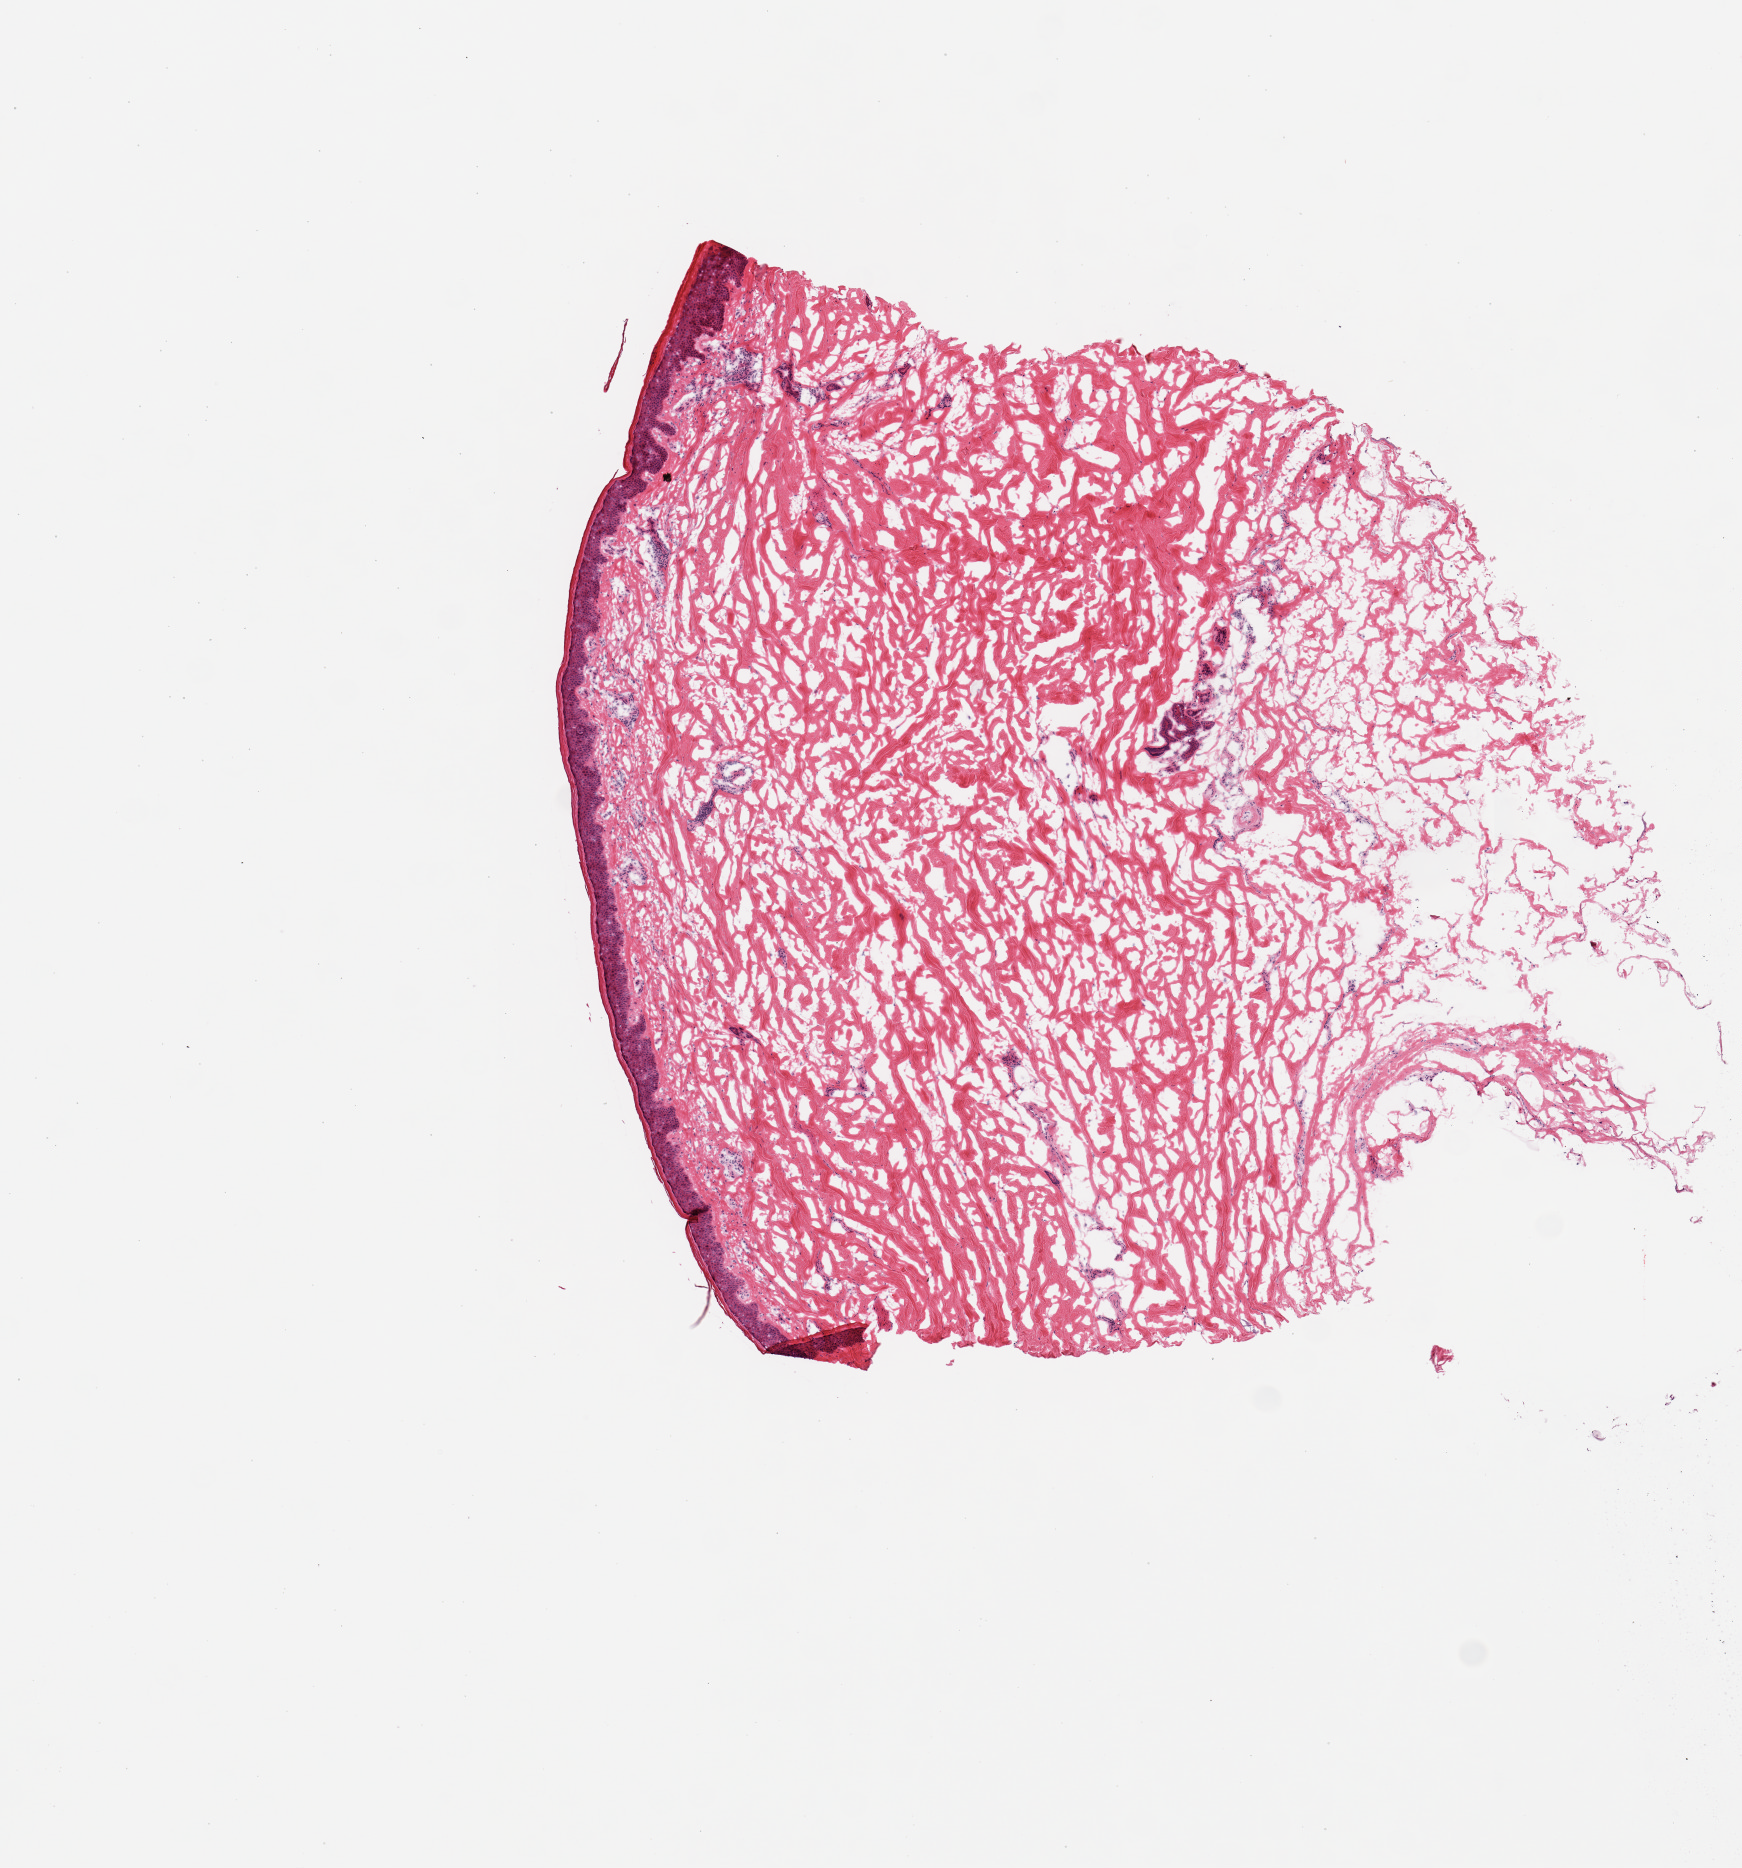
Hematoxylin and eosin (H&E) whole-slide image — low-resolution overview of the scanned area, about 6.9 x 7.4 mm (slide scanned at 20x). Donor sex: male.
Specimen: frozen section (dry ice); target tissue: skin of lower leg; donor tissue sample.